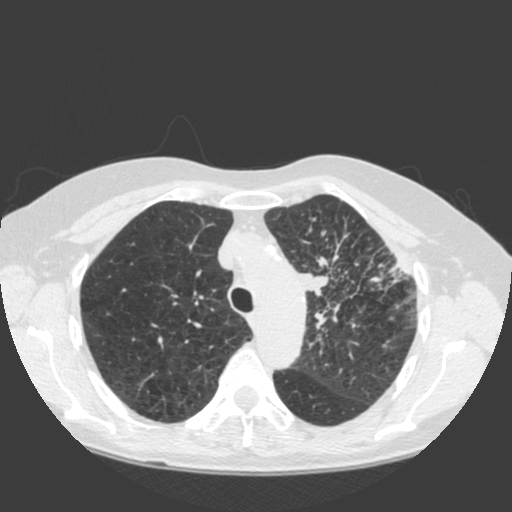
Low-dose screening chest CT, one axial slice; slice 142 of 184 in the series (ordered by position); 120 kVp; lung window (W 1500 / L -600 HU); 512 × 512 image matrix, field of view 350 × 350 mm.
Structures marked on this image (outlined manually by an expert reader):
- lesion 1 (tumor, hilum of left lung): bounding box [x1, y1, x2, y2] px = [296, 271, 329, 296]